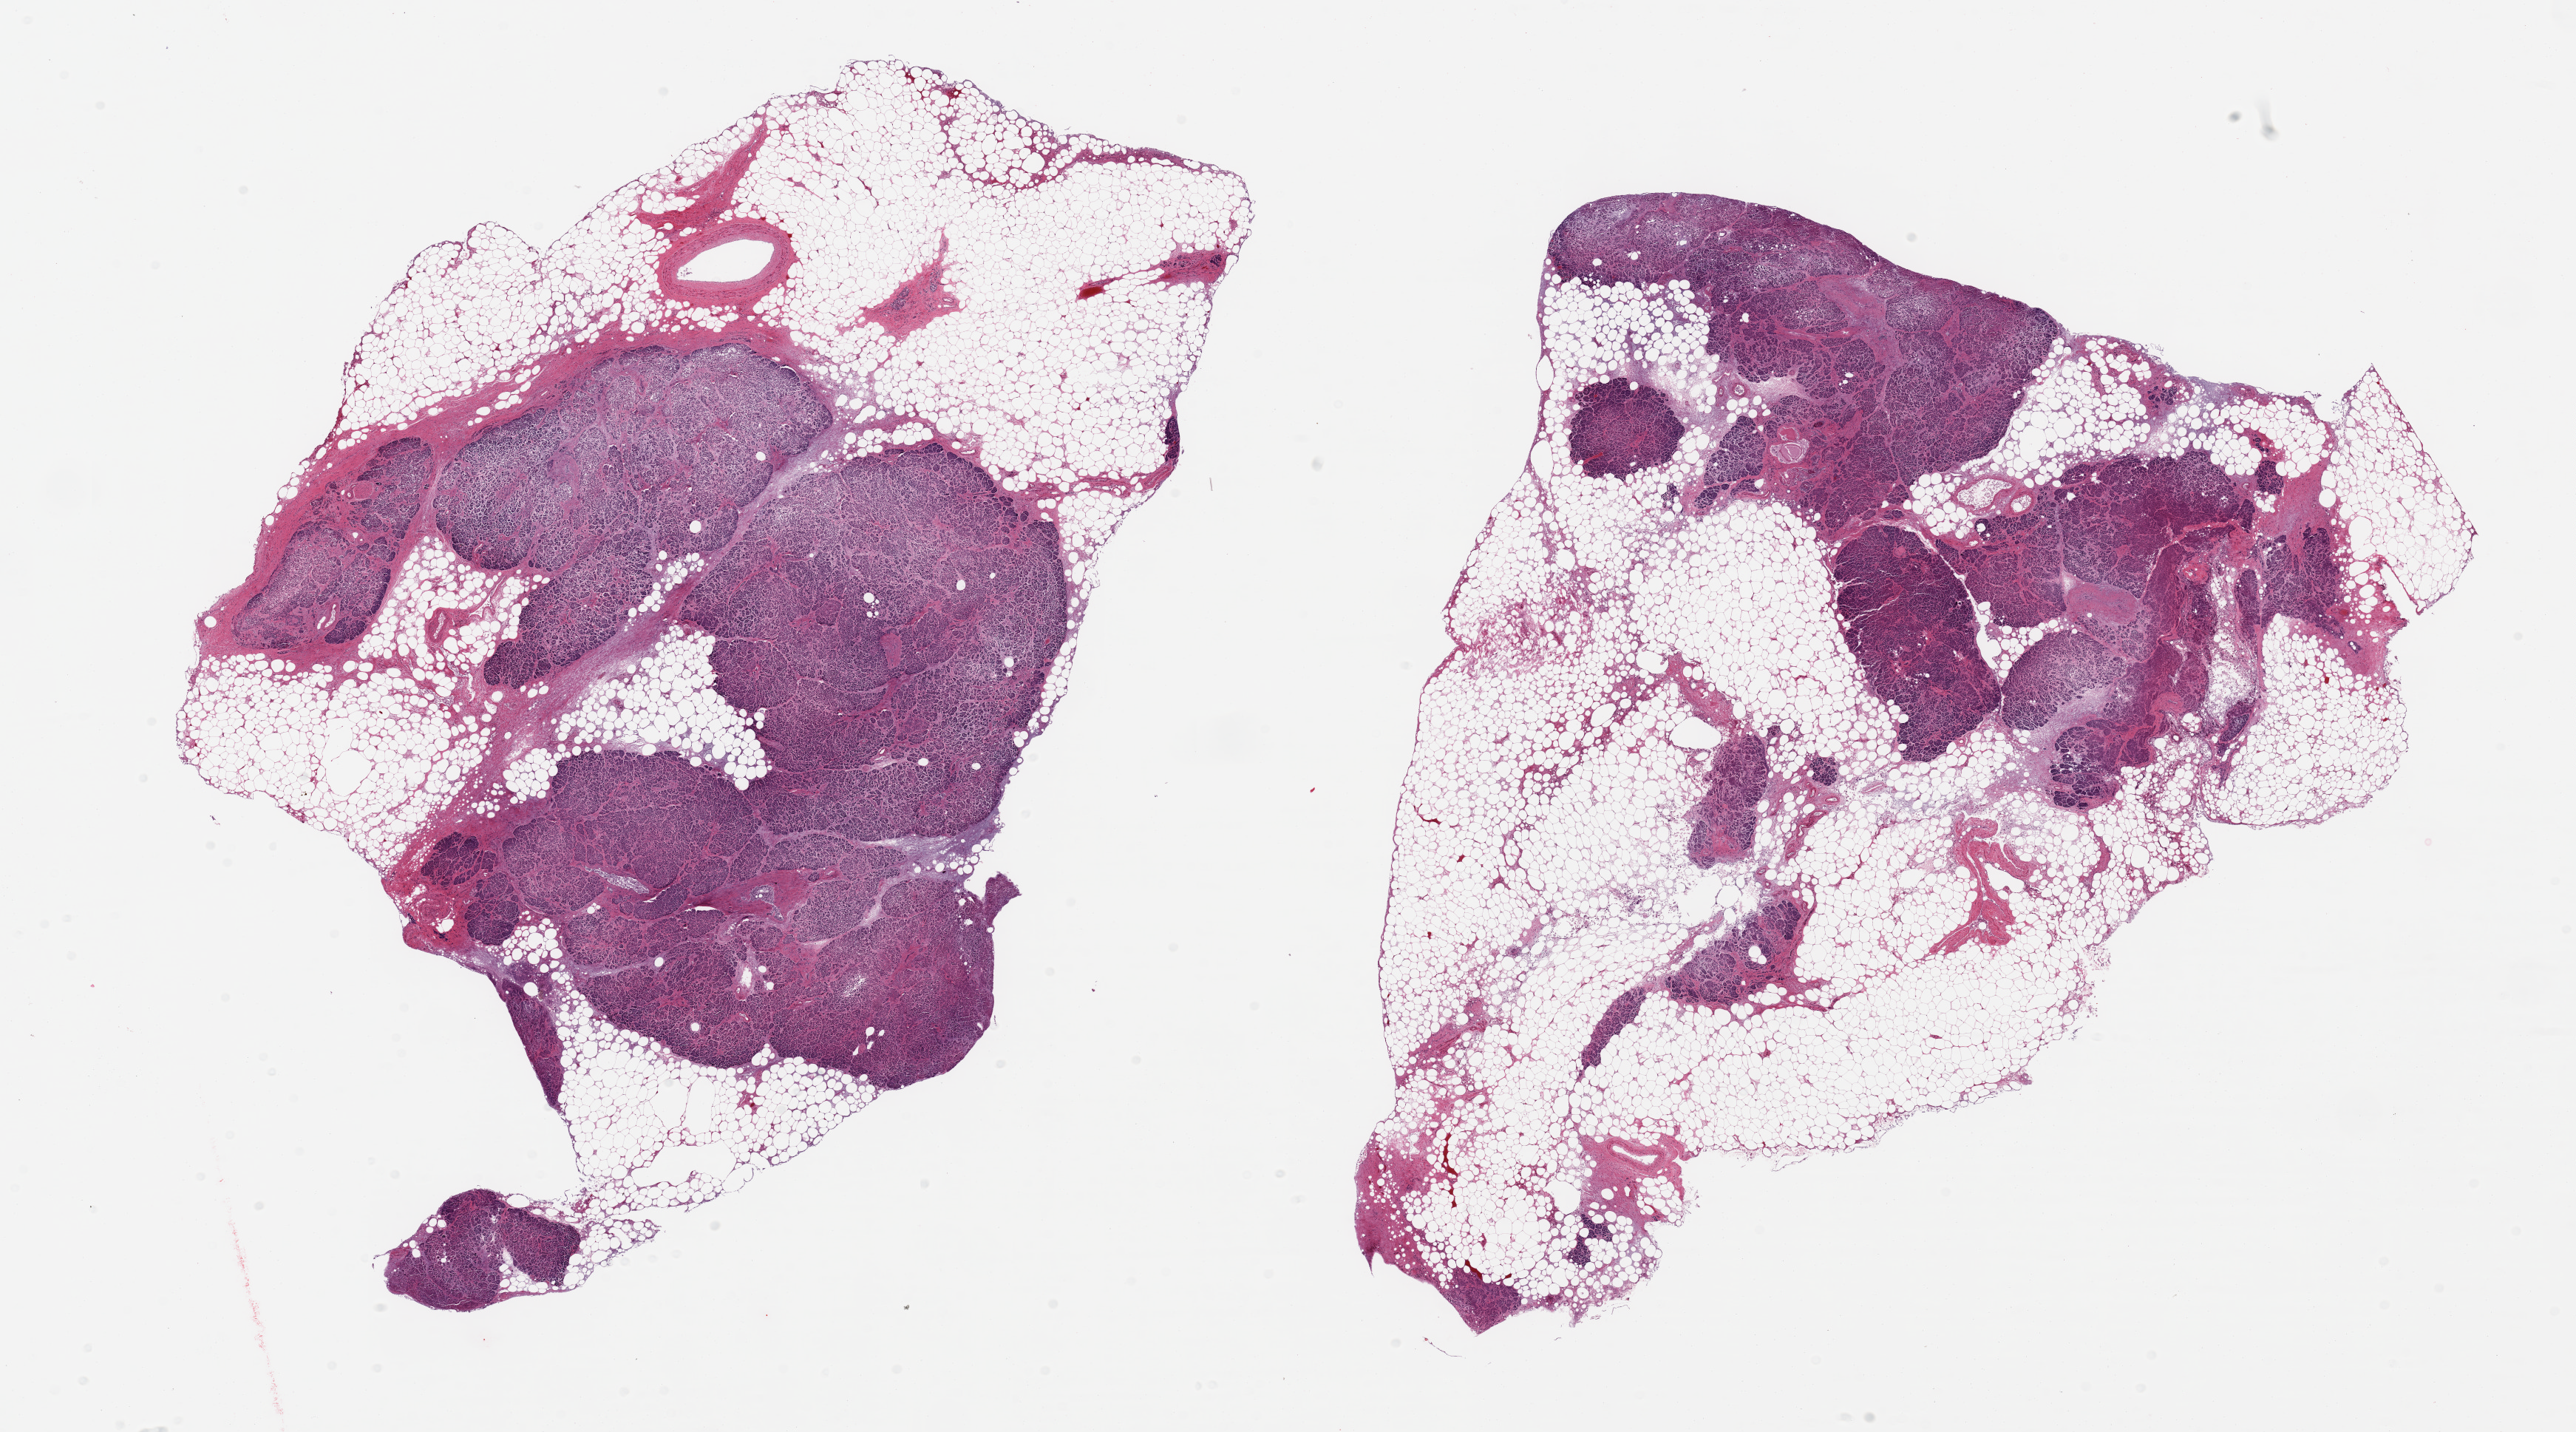
Digitized hematoxylin and eosin (H&E)-stained section — low-resolution overview of the scanned area, about 27.6 x 15.3 mm, PAXgene-fixed paraffin-embedded (PFPE) section, target tissue: pancreas, tissue donor sample. Donor: male.
Pathologist's review note for this sample: 2 pieces, ~50% adherent/interstitial fat; advanced saponification, Islets not visible.